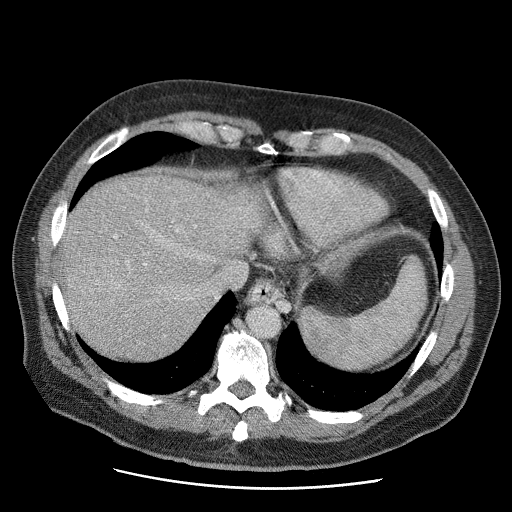
Contrast-enhanced abdominal CT (liver protocol), one axial slice. Slice 51 of 81 in the series (ordered by position). Reconstruction kernel STANDARD. 120 kVp. Soft-tissue window (W 400 / L 40 HU). 2.5 mm slice thickness. 512 × 512 image matrix, field of view 380 × 380 mm. From the clinical record (not read from this slice): diagnosis: hepatocellular carcinoma (patient treated with transarterial chemoembolisation; whether this scan precedes or follows treatment is not stated here); TNM stage (as recorded): Stage-IIIA; Child-Pugh class: A.
Structures marked on this image (semi-automatically segmented with operator editing):
- liver parenchyma outside the tumour (the mass and vessels are separate outlines, so this box may not span the whole liver): bounding box <60,174,272,360> (left, top, right, bottom; pixels)
- mass: <64,239,130,302>
- liver vessels: <114,230,200,266>